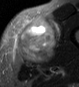
MRI of an extremity soft-tissue mass, one axial slice. Slice 25 of 45 in the series (ordered by position). STIR. MR volume resampled by the dataset authors to the PET/CT grid (not the native acquisition matrix). 3.27 mm slice thickness. 79 × 87 image matrix, field of view 77 × 85 mm. Male patient. Case-level facts recorded for this patient, not image findings: histological type: pleiomorphic leiomyosarcoma; grade: high; site of the primary tumour: left thigh.
Structures marked on this image (expert contour drawn on MRI and transferred to this co-registered scan by the dataset authors):
- gross tumour volume including surrounding oedema: bounding box <15,16,60,63> (left, top, right, bottom; pixels)
- gross tumour volume (mass): <15,18,57,63>